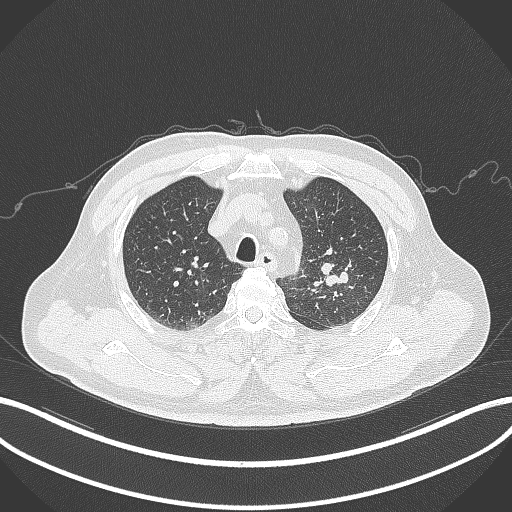
Chest CT, one axial slice. Reconstruction kernel B70f. 120 kVp. Lung window (W 1500 / L -600 HU). 512 × 512 image matrix, field of view 400 × 400 mm. Male patient, age 67 years. From the clinical record (not read from this slice): clinical TNM (as recorded): T2a N1 M0; histopathological grade: G3.
Outlined on this slice (bounding box drawn by a radiologist):
- lung tumour (recorded histology: adenocarcinoma): box from (x=317, y=258) to (x=351, y=289) px